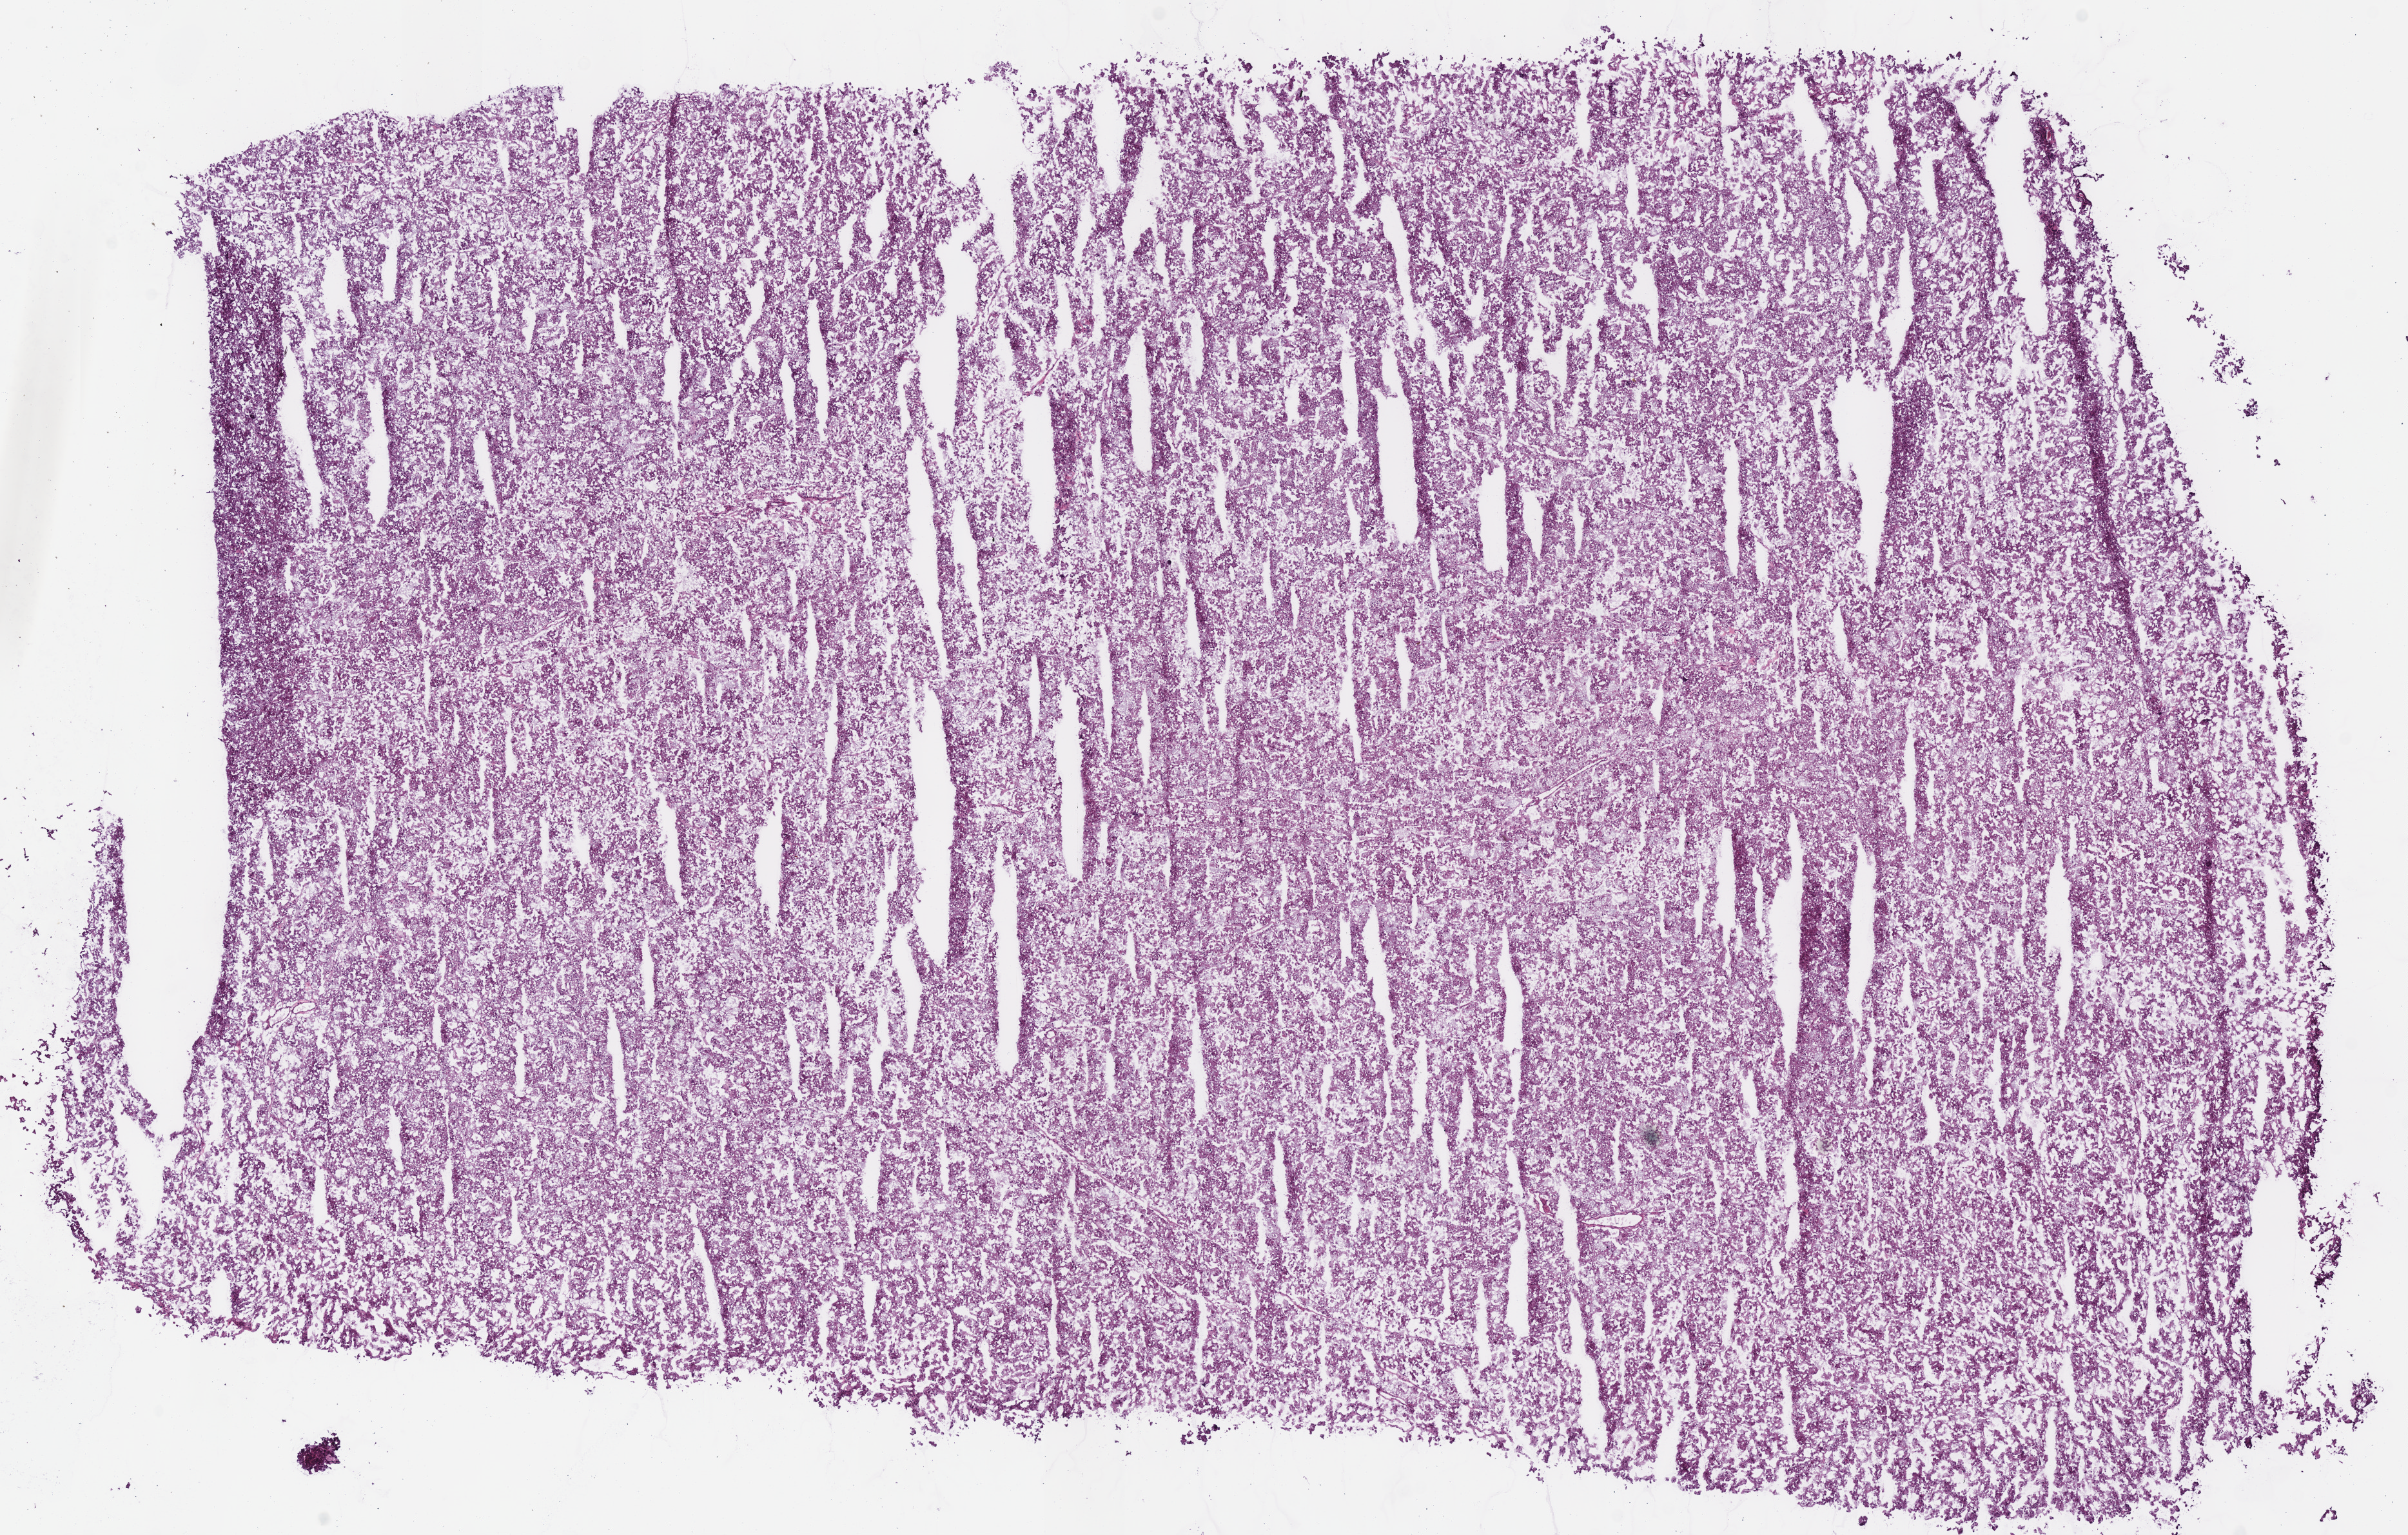
Digitized H&E-stained tissue section (whole slide), whole scanned area (about 14.7 x 9.4 mm, slide scanned at 40x) shown as a low-resolution overview, frozen section from the bottom of the tissue portion, primary tumour sample from the kidney. Male, age 58 years at initial diagnosis. Slide review estimates, as recorded: tumour cells 90%, tumour nuclei 90%, normal cells 0%, stromal cells 10%, necrosis 0%.
TNM: T1b NX M0. Histologic diagnosis: Renal cell carcinoma, chromophobe type. AJCC pathologic stage: I.